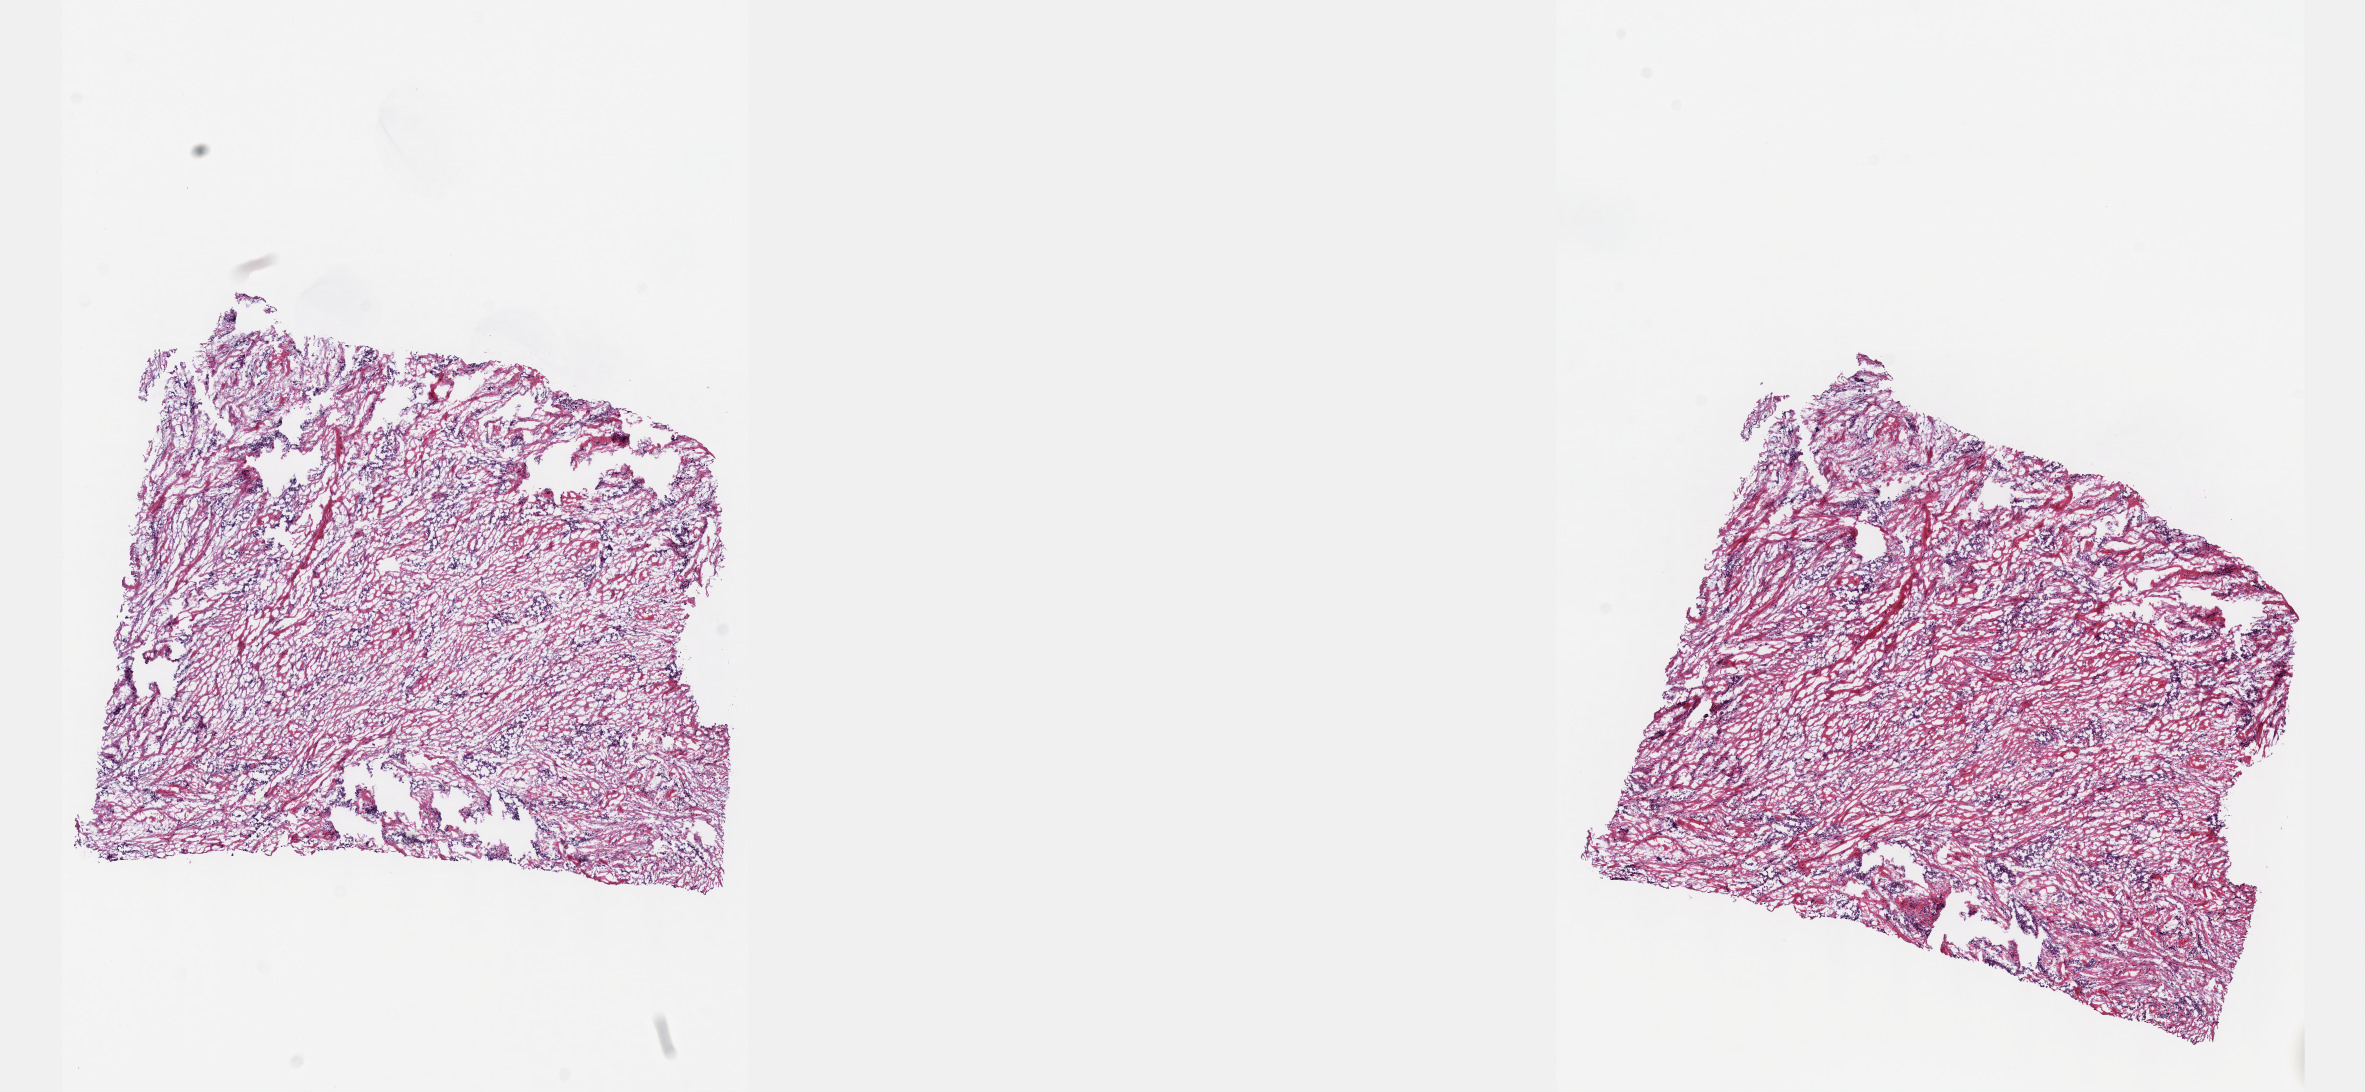
Digitized Hematoxylin and eosin (H&E) stained tissue section (whole slide) — low-resolution overview of the scanned area, about 19.1 x 8.8 mm. Frozen section from the top of the tissue portion. Sample: primary tumour, mesothelium. Male patient; age at initial diagnosis 50 years. Composition of this section per pathologist review: tumour cells 100%, tumour nuclei 65%, normal cells 0%, stromal cells 0%, necrosis 0%. Infiltration values recorded for this section: lymphocyte infiltration 2%, monocyte infiltration 0%, neutrophil infiltration 0%.
Laterality: right. AJCC pathologic stage: III (5th edition). TNM: T3 N0 M0. Histologic diagnosis: Epithelioid mesothelioma, malignant (pleura, NOS).